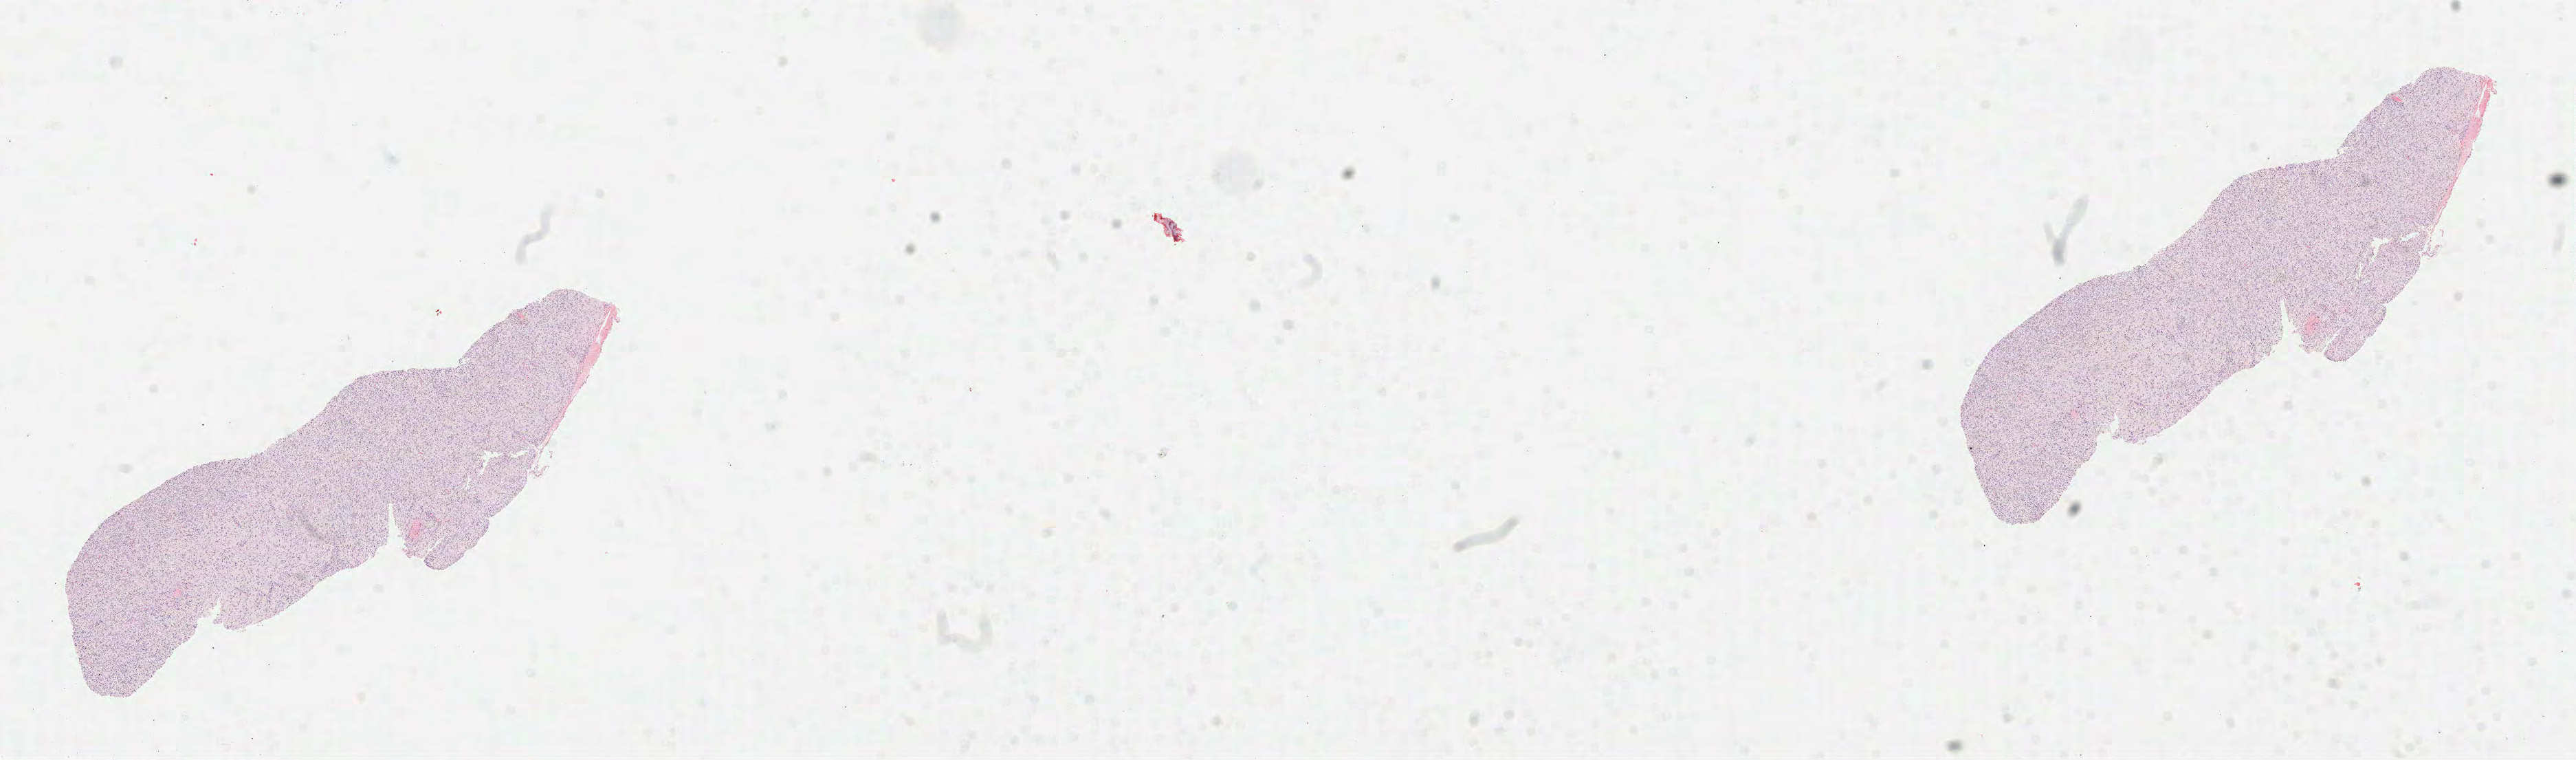
Whole-slide histology image, Hematoxylin and eosin (H&E) stained — whole scanned area (about 30.2 x 8.9 mm, from a 40x scan) shown as a low-resolution overview. FFPE section. Sample: primary tumour, brain. Male patient; age at initial diagnosis 51 years.
Pathologic diagnosis: Glioblastoma.